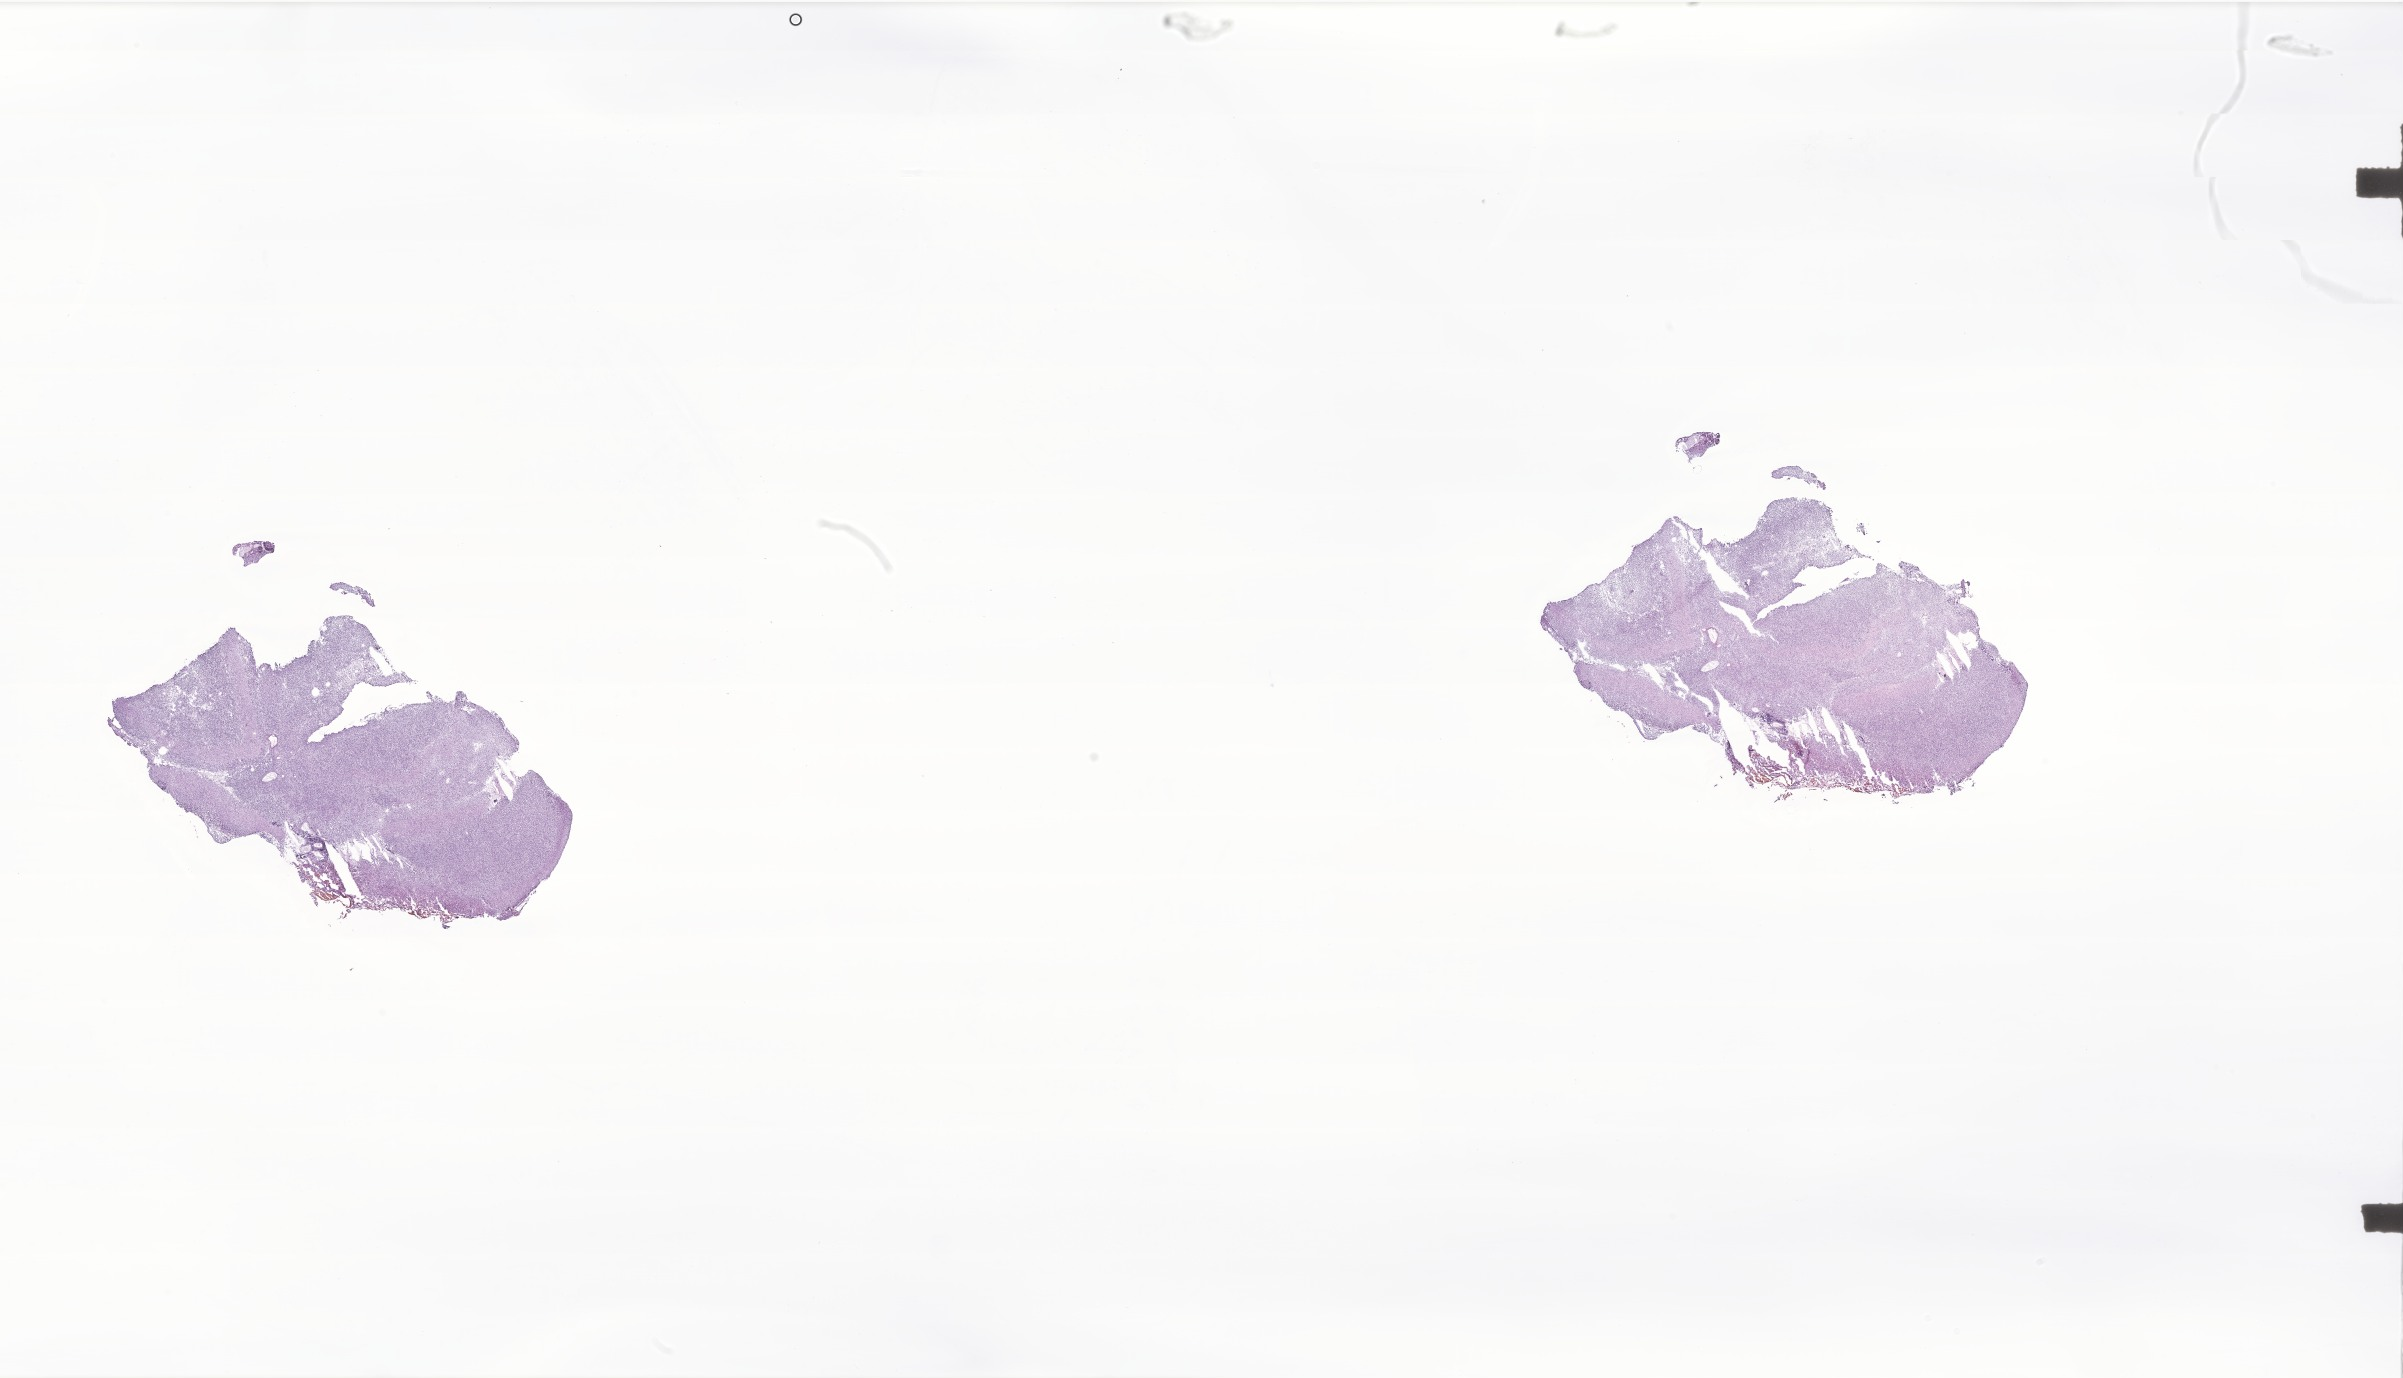
Hematoxylin and eosin (H&E) whole-slide image of tumor tissue from the central nervous system — a low-resolution overview of the entire scanned area, about 40.5 x 23.2 mm; frozen section (OCT-embedded). Male patient, age 172 months (14 years 4 months).
- diagnosis (ICD-O-3 morphology term): Medulloblastoma, NOS